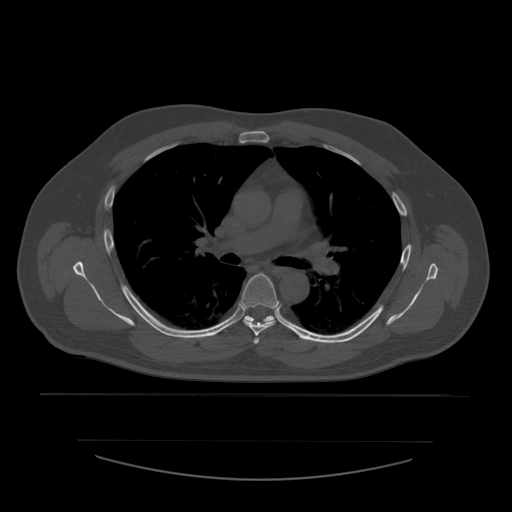
CT including the spine, one axial slice. Slice 393 of 532 in the series (ordered by position). Bone window (W 1800 / L 400 HU). 512 × 512 image matrix, field of view 441 × 441 mm. Patient age 44 years. From the clinical record (not read from this slice): primary cancer: soft tissue sarcoma.
Outlined on this slice (semi-automatically segmented with operator editing):
- T4 vertebra: bounding box [x1, y1, x2, y2] px = [254, 338, 260, 344]
- T5 vertebra: [241, 273, 280, 336]
- T6 vertebra: [222, 316, 274, 331]